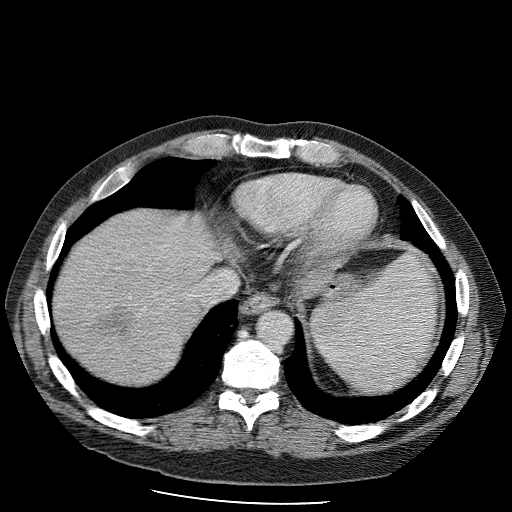
Contrast-enhanced abdominal CT (liver protocol), one axial slice. Position 89 of 98 along the scan axis. Reconstruction kernel STANDARD. Soft-tissue window (W 400 / L 40 HU). 512 × 512 image matrix, field of view 400 × 400 mm. From the clinical record (not read from this slice): diagnosis: hepatocellular carcinoma (patient treated with transarterial chemoembolisation; whether this scan precedes or follows treatment is not stated here); TNM stage (as recorded): Stage-II; Child-Pugh class: B; tumour nodularity: uninodular.
Structures marked on this image (semi-automatically segmented with operator editing):
- liver parenchyma outside the tumour (the mass and vessels are separate outlines, so this box may not span the whole liver): bounding box [x1, y1, x2, y2] px = [54, 210, 218, 378]
- mass: [84, 307, 135, 346]